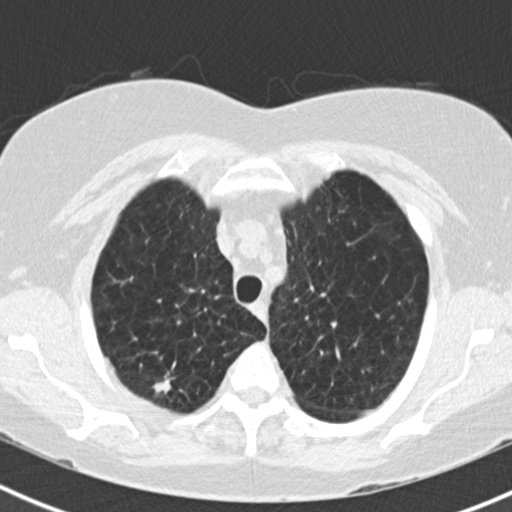
Low-dose screening chest CT, one axial slice. Position 141 of 180 along the scan axis. Reconstruction kernel B30f. Lung window (W 1500 / L -600 HU). 2 mm slice thickness. 512 × 512 image matrix, field of view 310 × 310 mm.
Structures marked on this image (manually delineated by an expert):
- lesion 1 (tumor, upper lobe of right lung): bounding box [x1, y1, x2, y2] px = [153, 376, 174, 394]